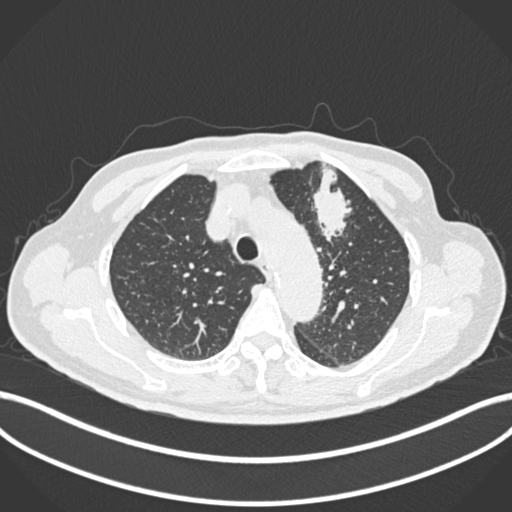
Chest CT, one axial slice; position 195 of 261 along the scan axis; 120 kVp; lung window (W 1500 / L -600 HU); 1 mm slice thickness; 512 × 512 image matrix. Patient: male, 74 years. From the clinical record (not read from this slice): clinical TNM (as recorded): T2b N0 M1c.
Outlined on this slice (rectangle marked by the reading radiologist):
- lung tumour (recorded histology: adenocarcinoma): box from (x=309, y=161) to (x=357, y=246) px